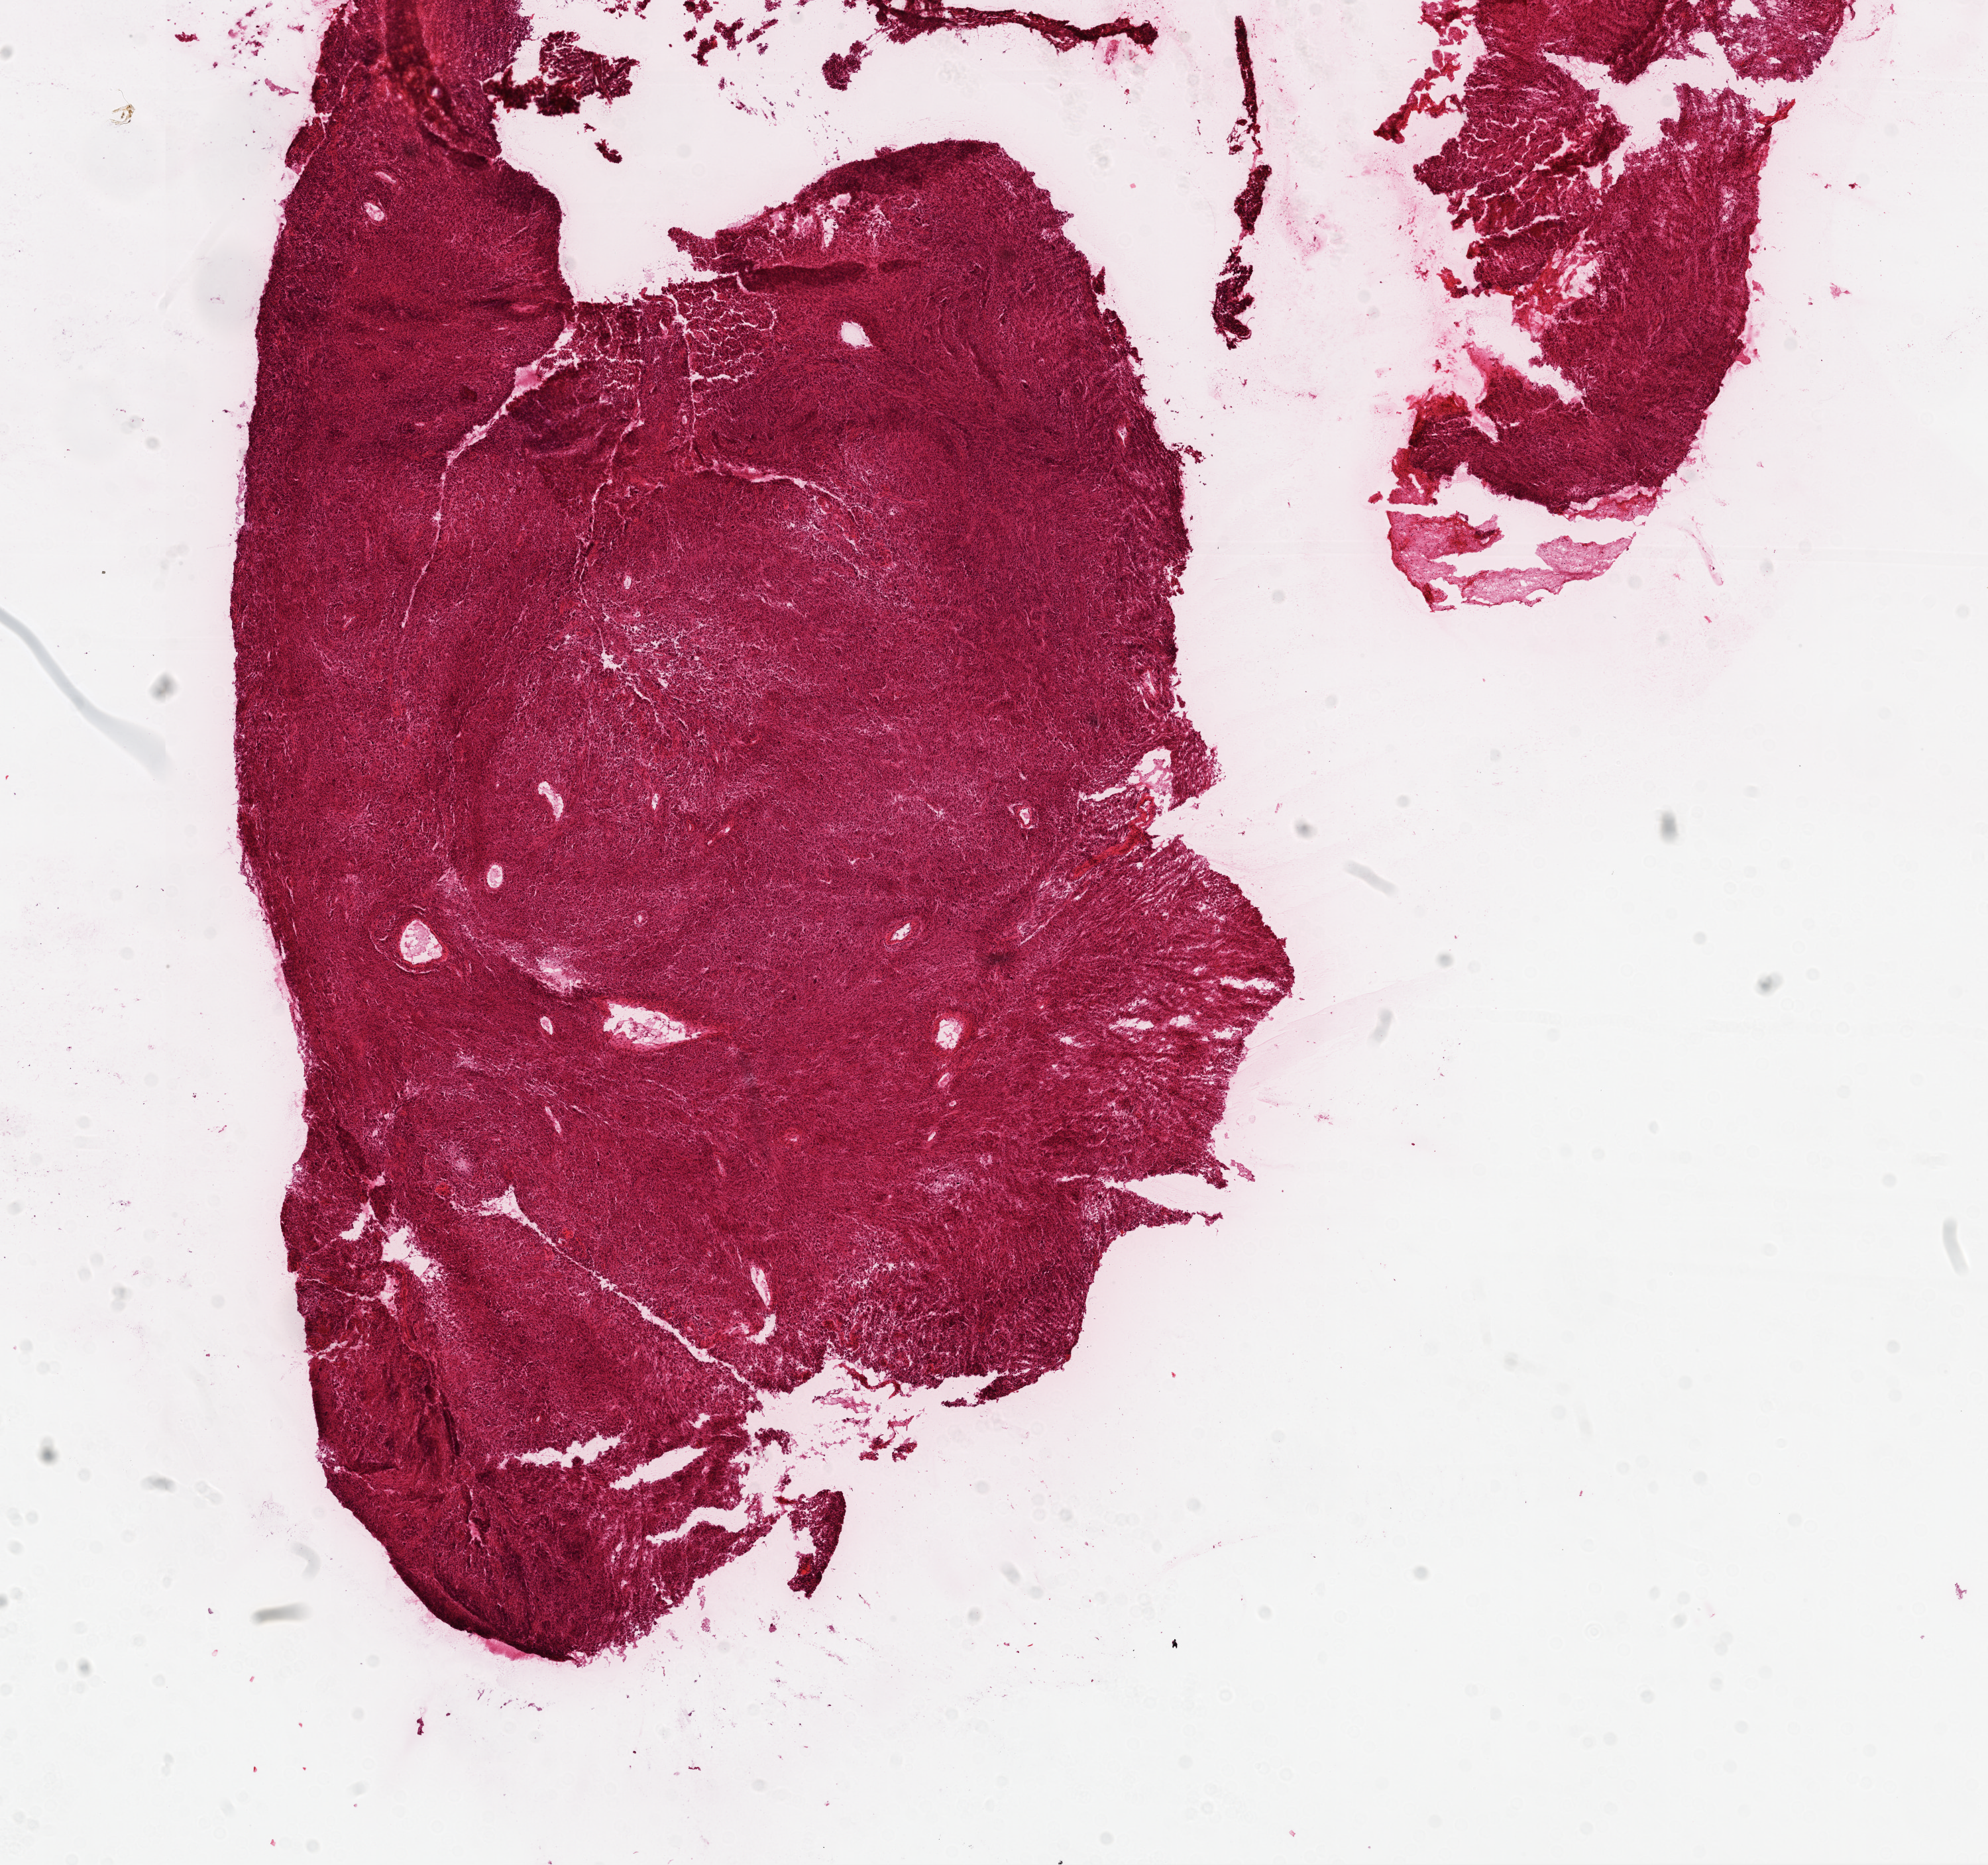
Whole-slide histology image, H&E-stained — whole scanned area (about 12.0 x 11.3 mm, from a 20x scan) shown as a low-resolution overview. Frozen section from the top of the tissue portion. Brain, primary tumour sample. Patient: male, age at initial diagnosis 60 years. Pathologist review of this section (percent, as recorded): tumour cells 100%, tumour nuclei 85%.
Histologic diagnosis: Glioblastoma.